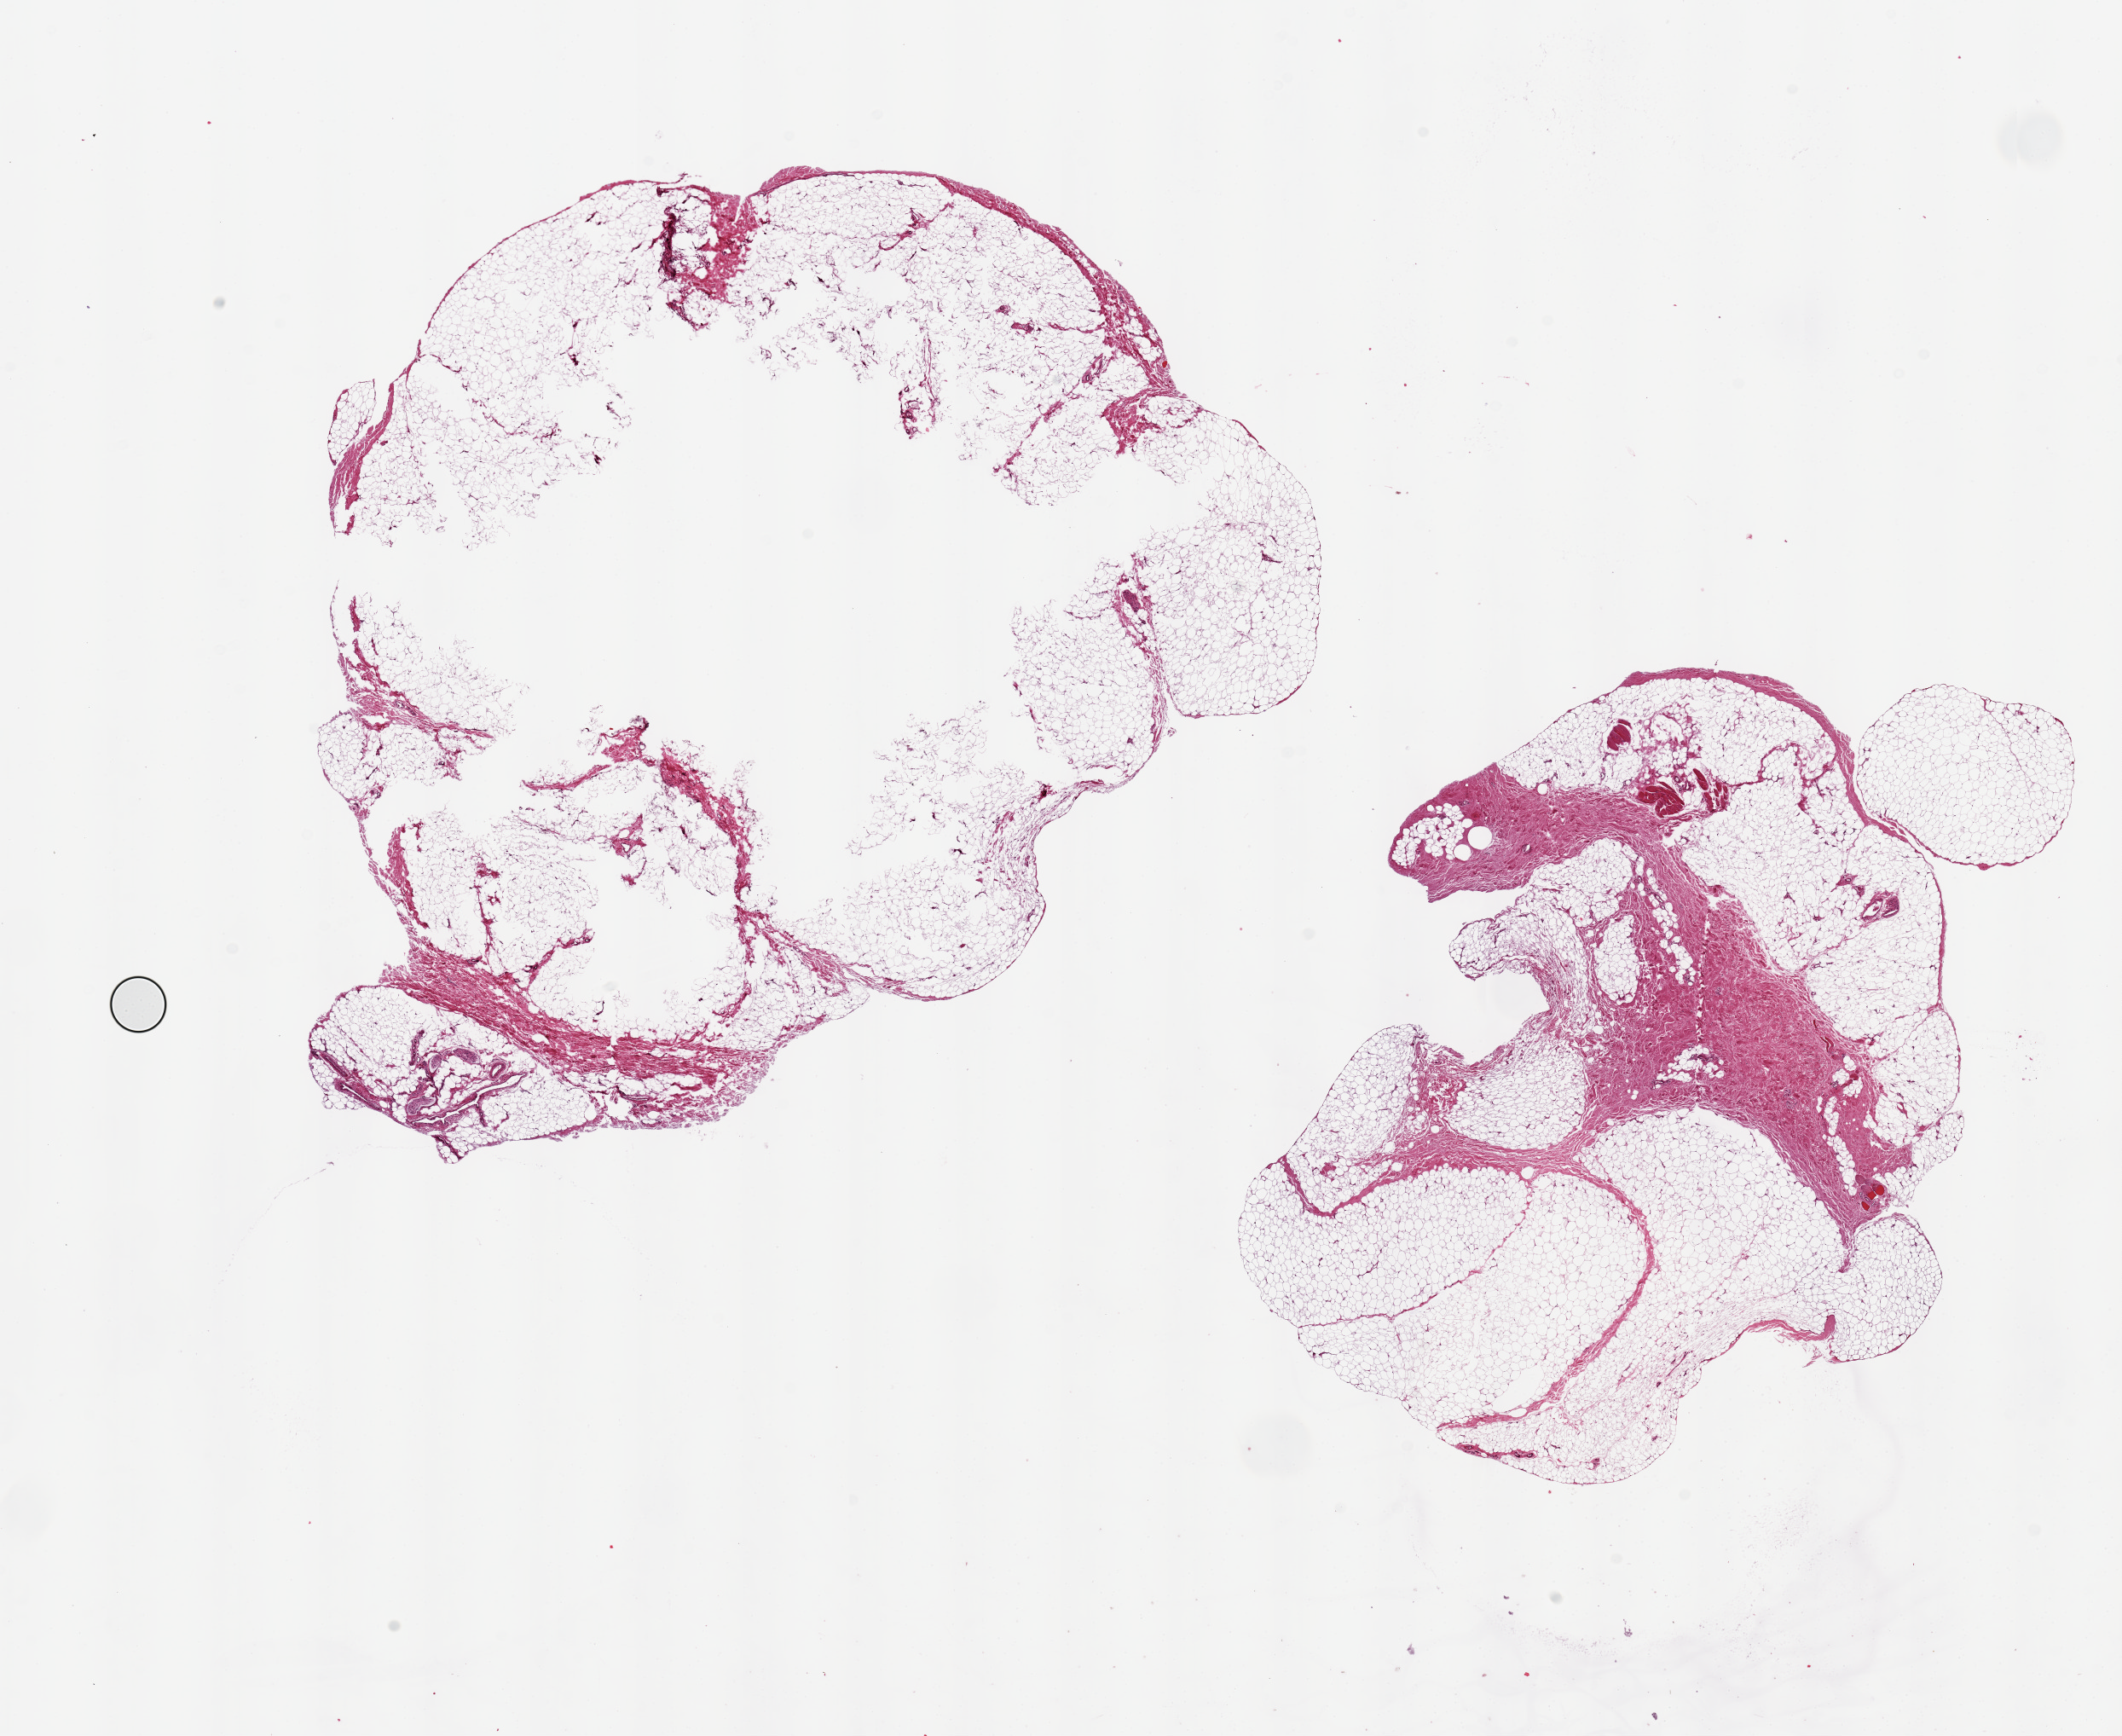
Digitized hematoxylin and eosin (H&E)-stained section — low-resolution overview of the scanned area, about 19.7 x 16.1 mm, PAXgene-fixed, paraffin-embedded tissue, sampled site (target tissue): thyroid, tissue donor sample. Male donor.
Pathologist's review note for this sample: Incorrect tissue, under-fixed adipose tissue only.